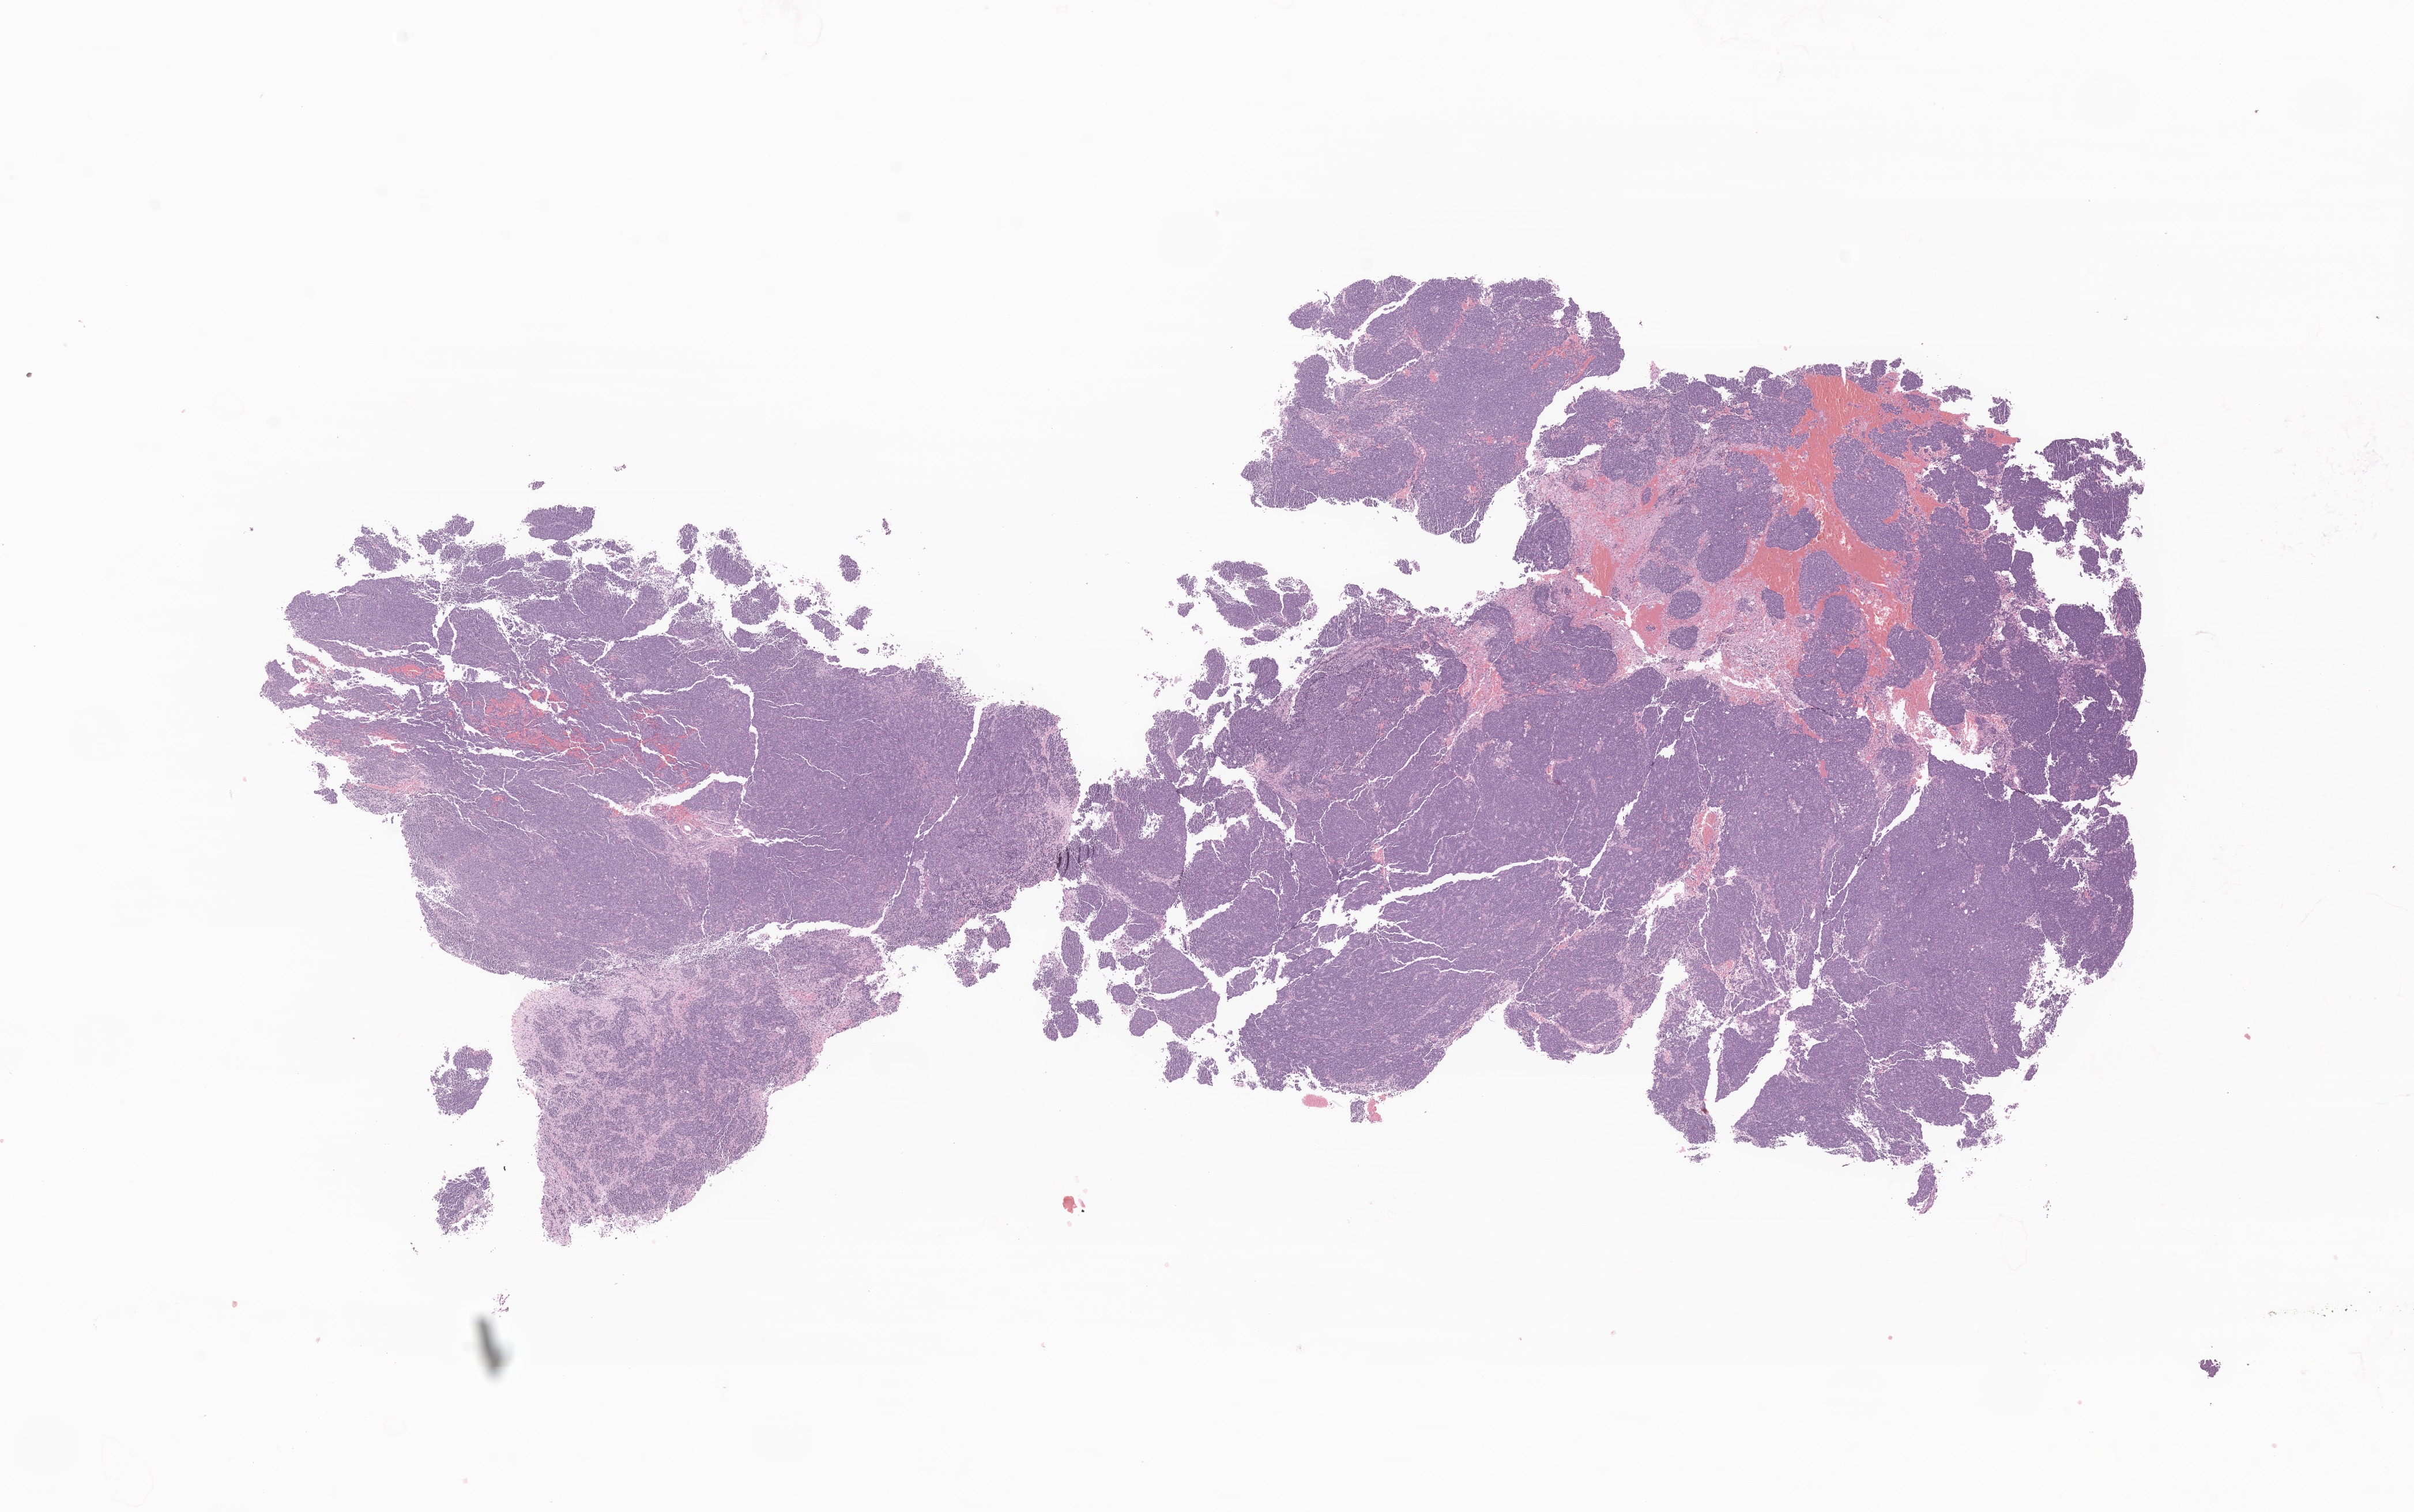
Digitized haematoxylin and eosin-stained section of tumor tissue from the brain — whole scanned area (about 17.7 x 11.1 mm) shown as a low-resolution overview; FFPE section. Male patient, age 123 months (10 years 3 months).
Recorded diagnosis: Medulloblastoma, NOS.